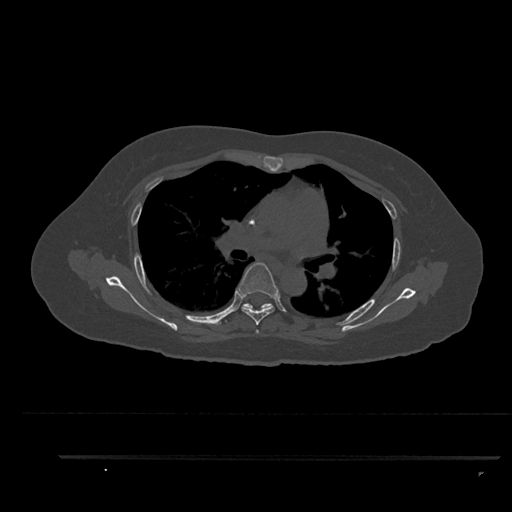
CT including the spine, one axial slice. Position 590 of 797 along the scan axis. 120 kVp. Bone window (W 1800 / L 400 HU). 512 × 512 image matrix. Female patient, age 44 years. Case-level facts recorded for this patient, not image findings: primary cancer: renal.
Outlined on this slice (semi-automatic segmentation, software-assisted and operator-edited):
- T4 vertebra: box from (x=256, y=329) to (x=259, y=334) px
- T5 vertebra: (x=238, y=262)–(x=280, y=325)
- T6 vertebra: (x=242, y=303)–(x=273, y=310)